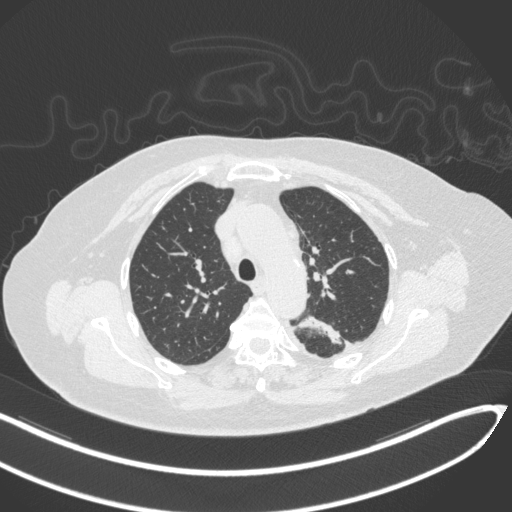
Chest CT, one axial slice; position 230 of 270 along the scan axis; 120 kVp; lung window (W 1500 / L -600 HU); 512 × 512 image matrix, field of view 400 × 400 mm. Patient: female, 76 years. From the clinical record (not read from this slice): clinical TNM (as recorded): T1c N0 M0.
Structures marked on this image (bounding box drawn by a radiologist):
- lung tumour (recorded histology: adenocarcinoma): box from (x=296, y=312) to (x=347, y=347) px